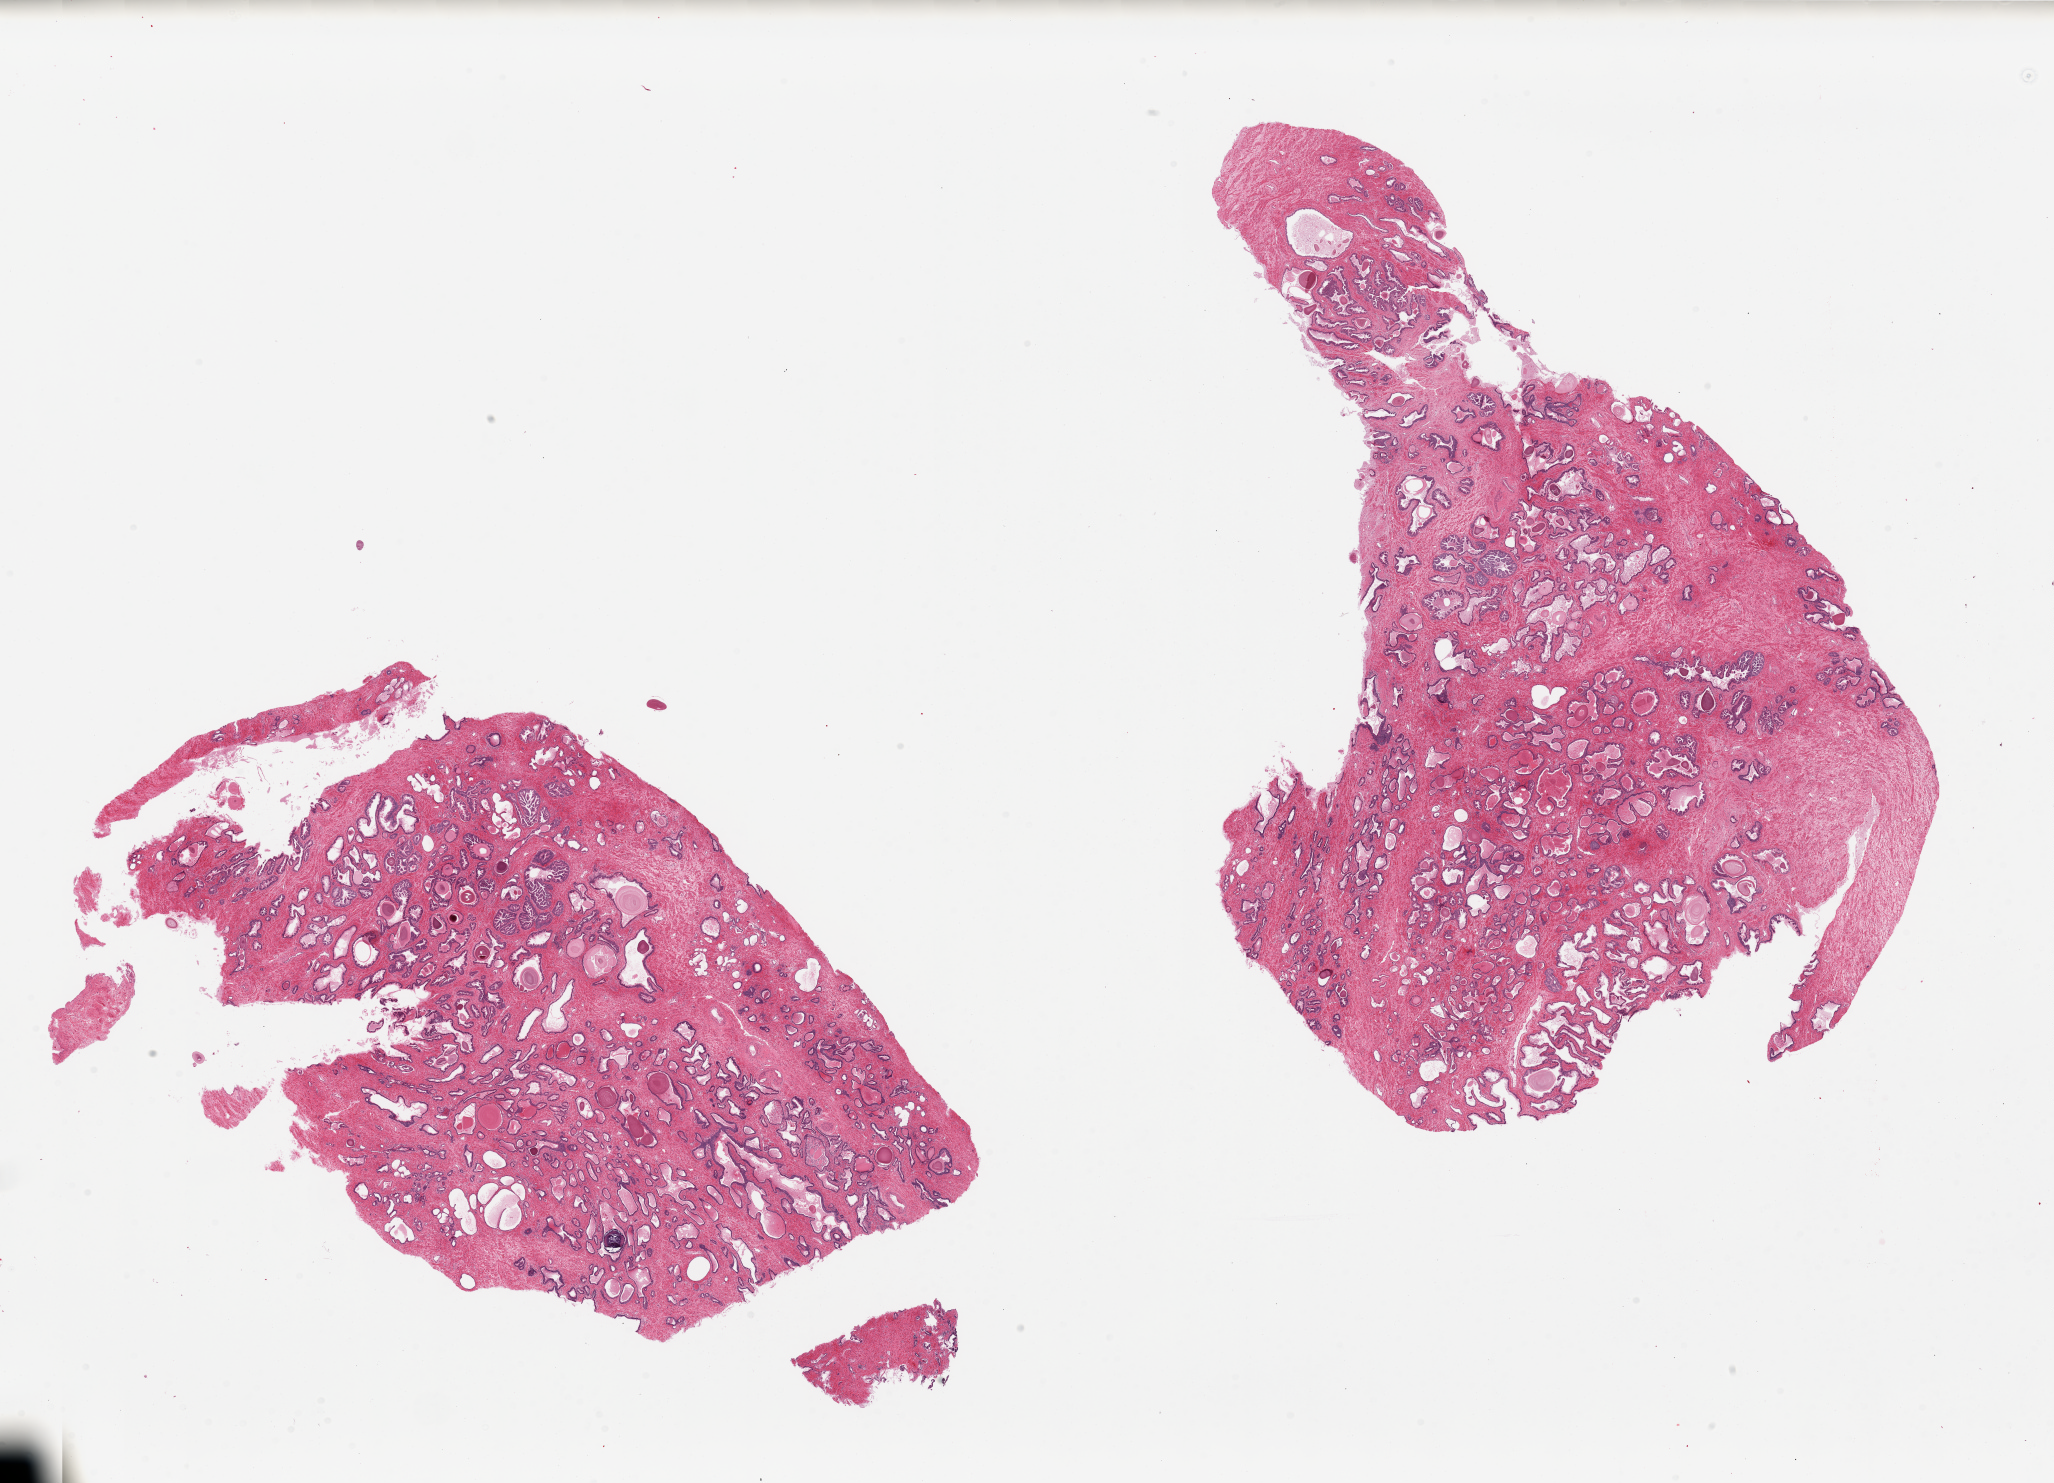
Whole-slide image, haematoxylin and eosin stain, brightfield — shown as a low-resolution overview of the whole scanned area (about 32.5 x 23.5 mm, acquisition: 20x scan). PAXgene-fixed, paraffin-embedded tissue. Target tissue: prostate. Tissue donor sample. Donor sex: male.
Reviewer comment on this tissue sample: 2 pieces; glandular hyperplasia.